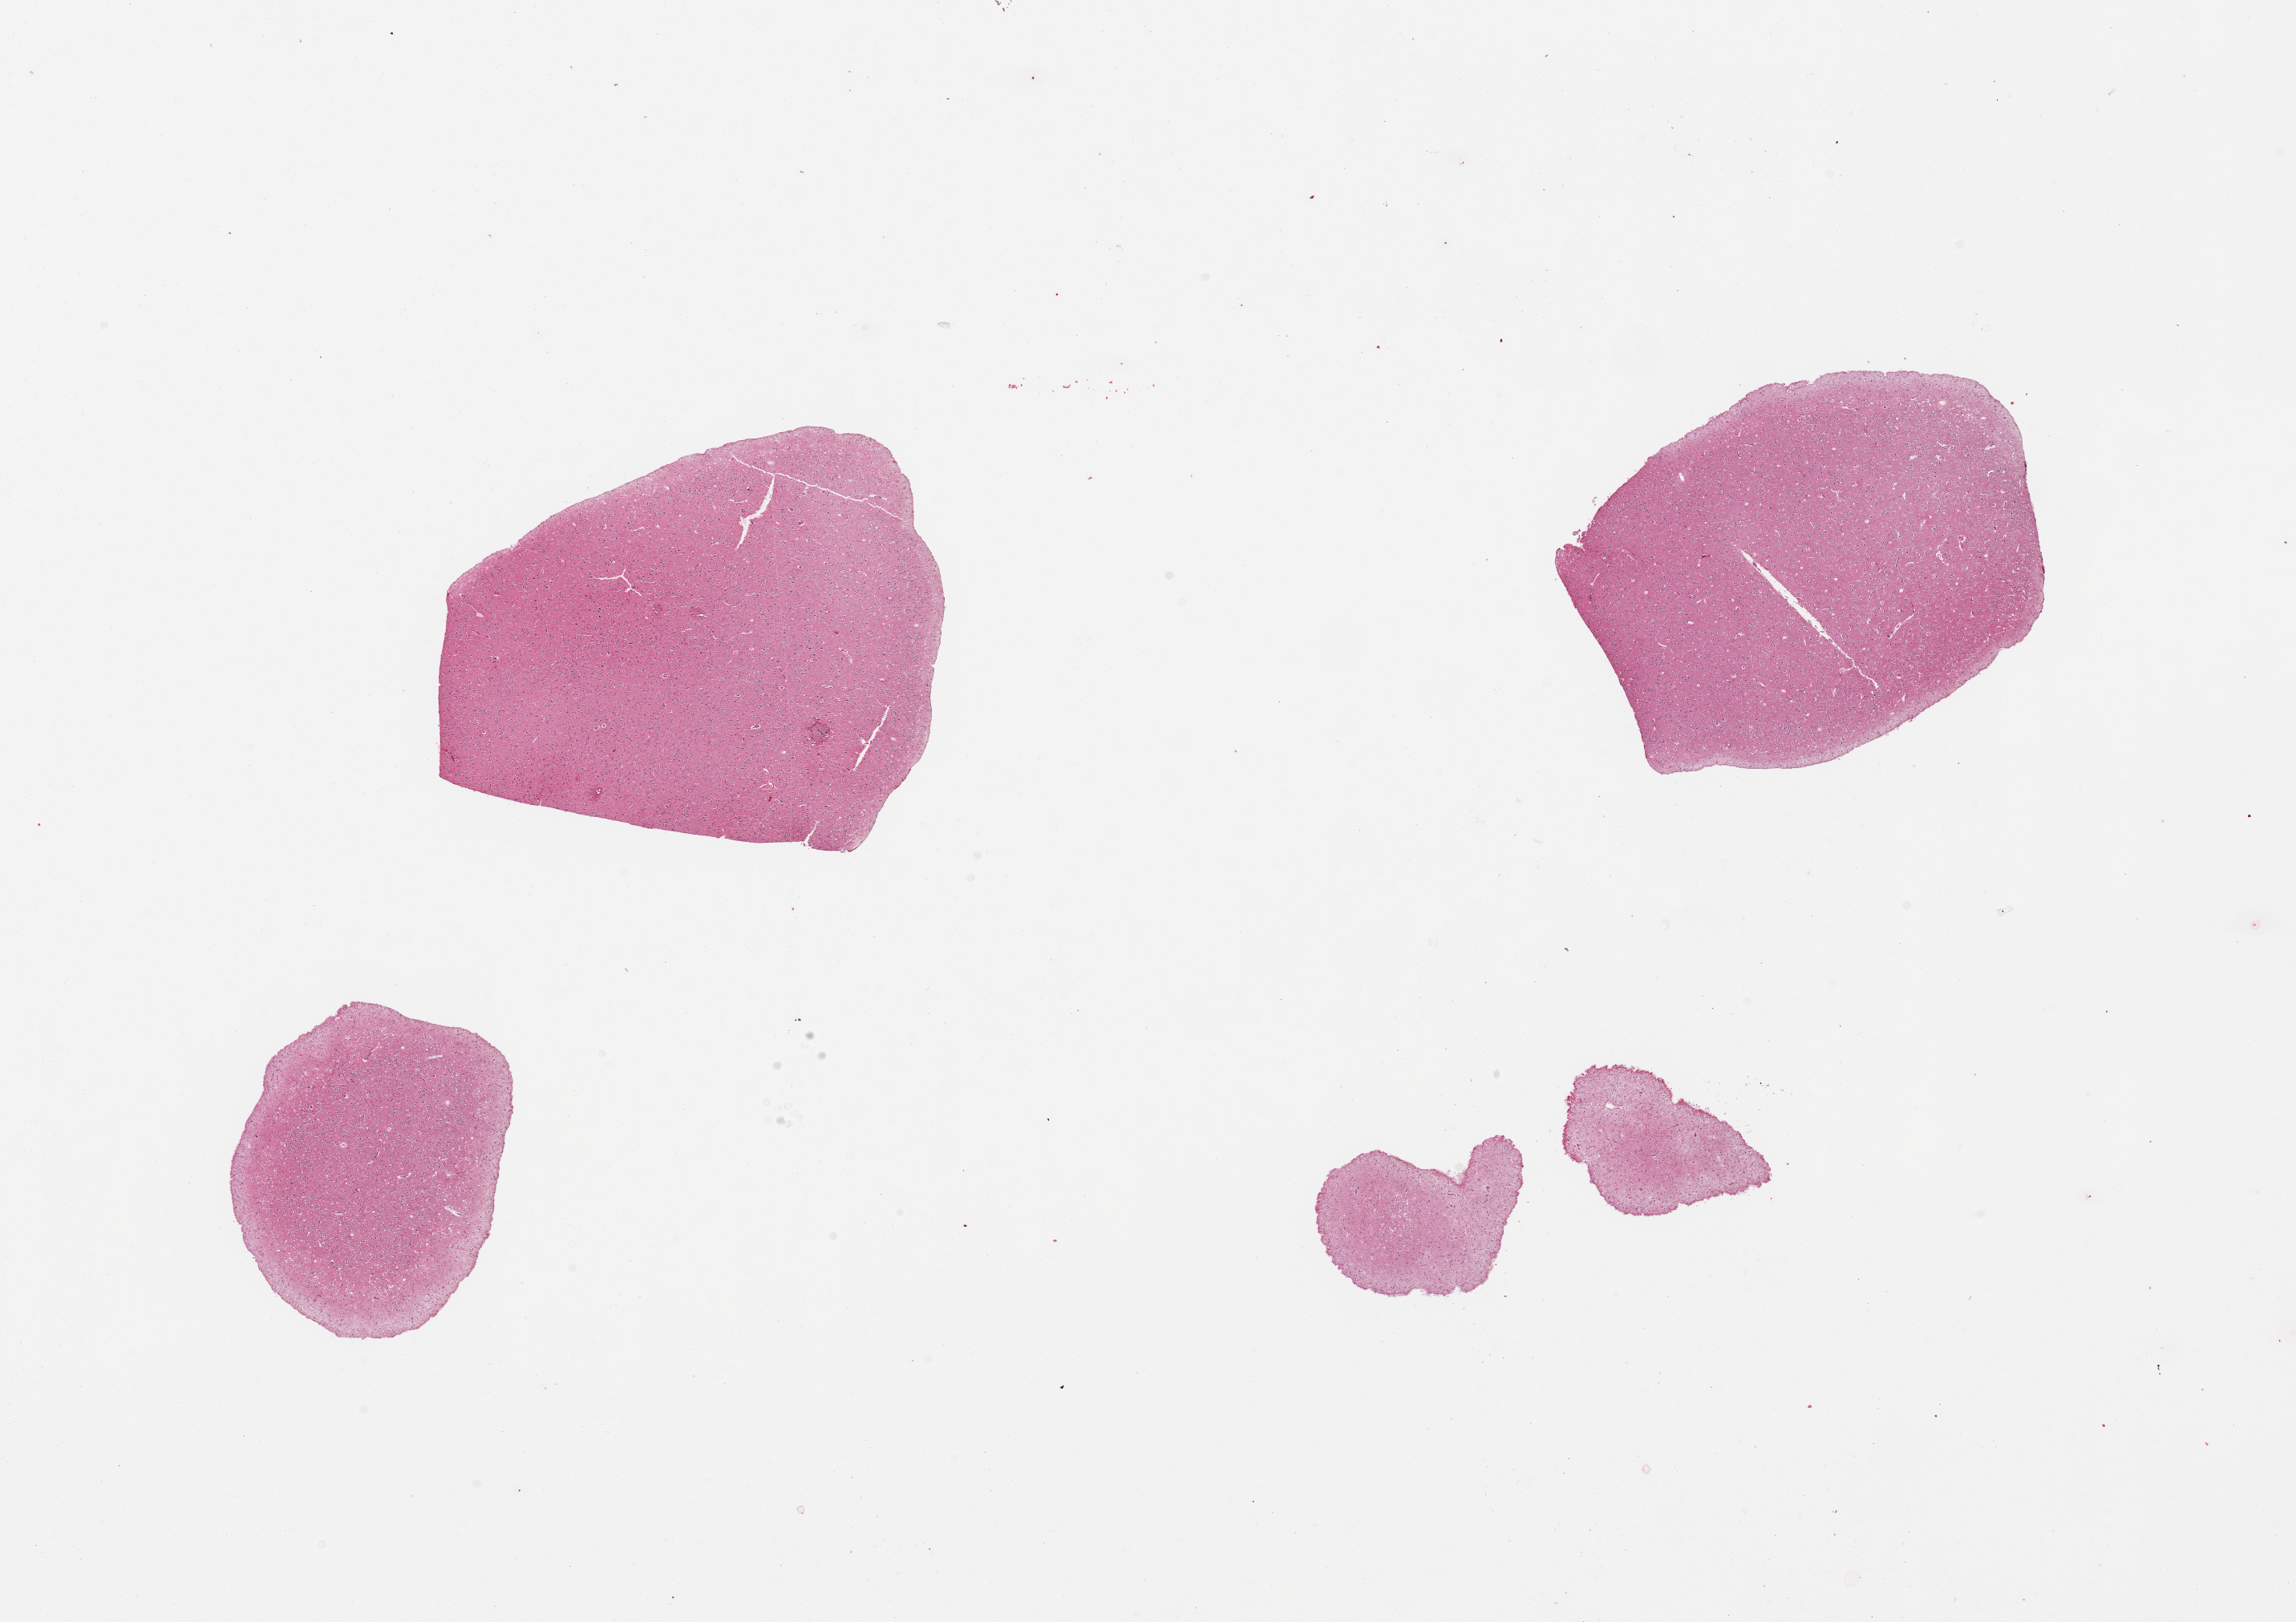
Whole-slide image, H&E stain — whole scanned area (about 22.6 x 16.0 mm, slide scanned at 20x) shown as a low-resolution overview, PAXgene-fixed paraffin-embedded (PFPE) section, section of cerebral cortex (target tissue), tissue donor sample.
* reviewer comment on this tissue sample: 4 pieces